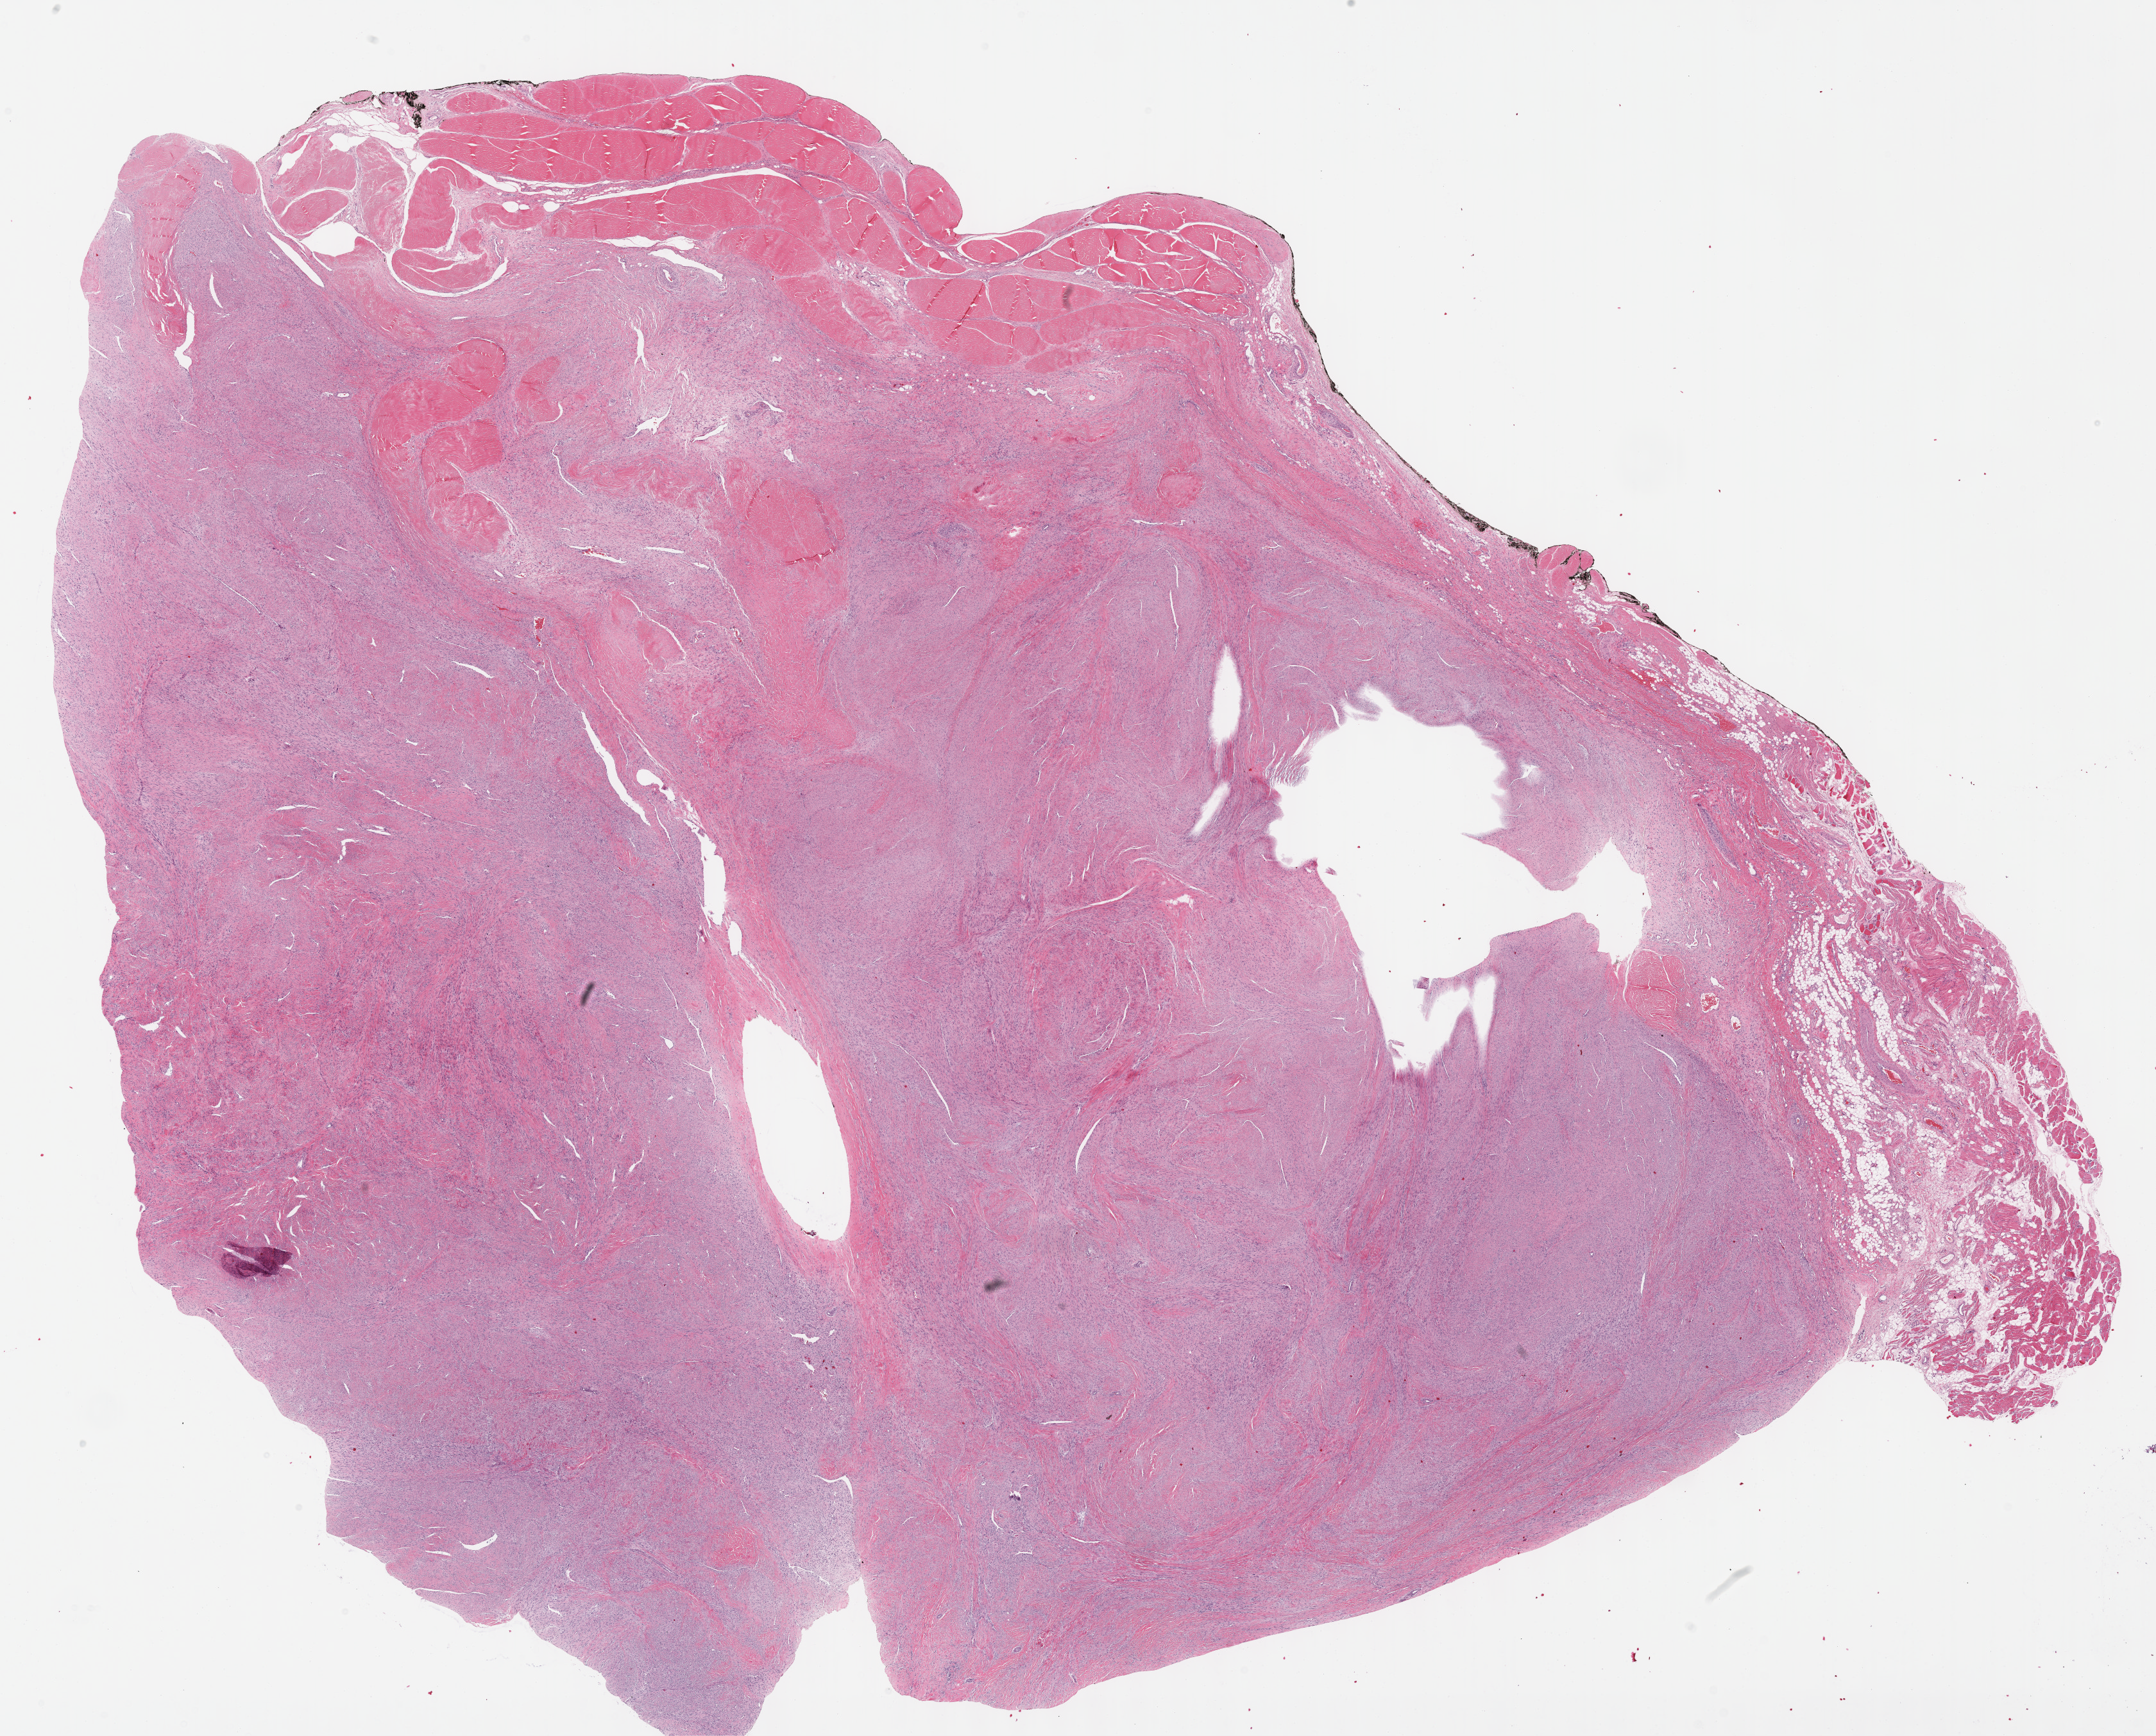
Digitized H&E tissue section (whole slide), shown as a low-resolution overview of the whole scanned area (about 27.2 x 21.9 mm, slide scanned at 40x), formalin-fixed paraffin-embedded (FFPE) diagnostic section, primary tumour sample from the connective, subcutaneous and other soft tissues. Patient: male, age at initial diagnosis 81 years.
Pathologic diagnosis: Dedifferentiated liposarcoma (connective, subcutaneous and other soft tissues of pelvis).